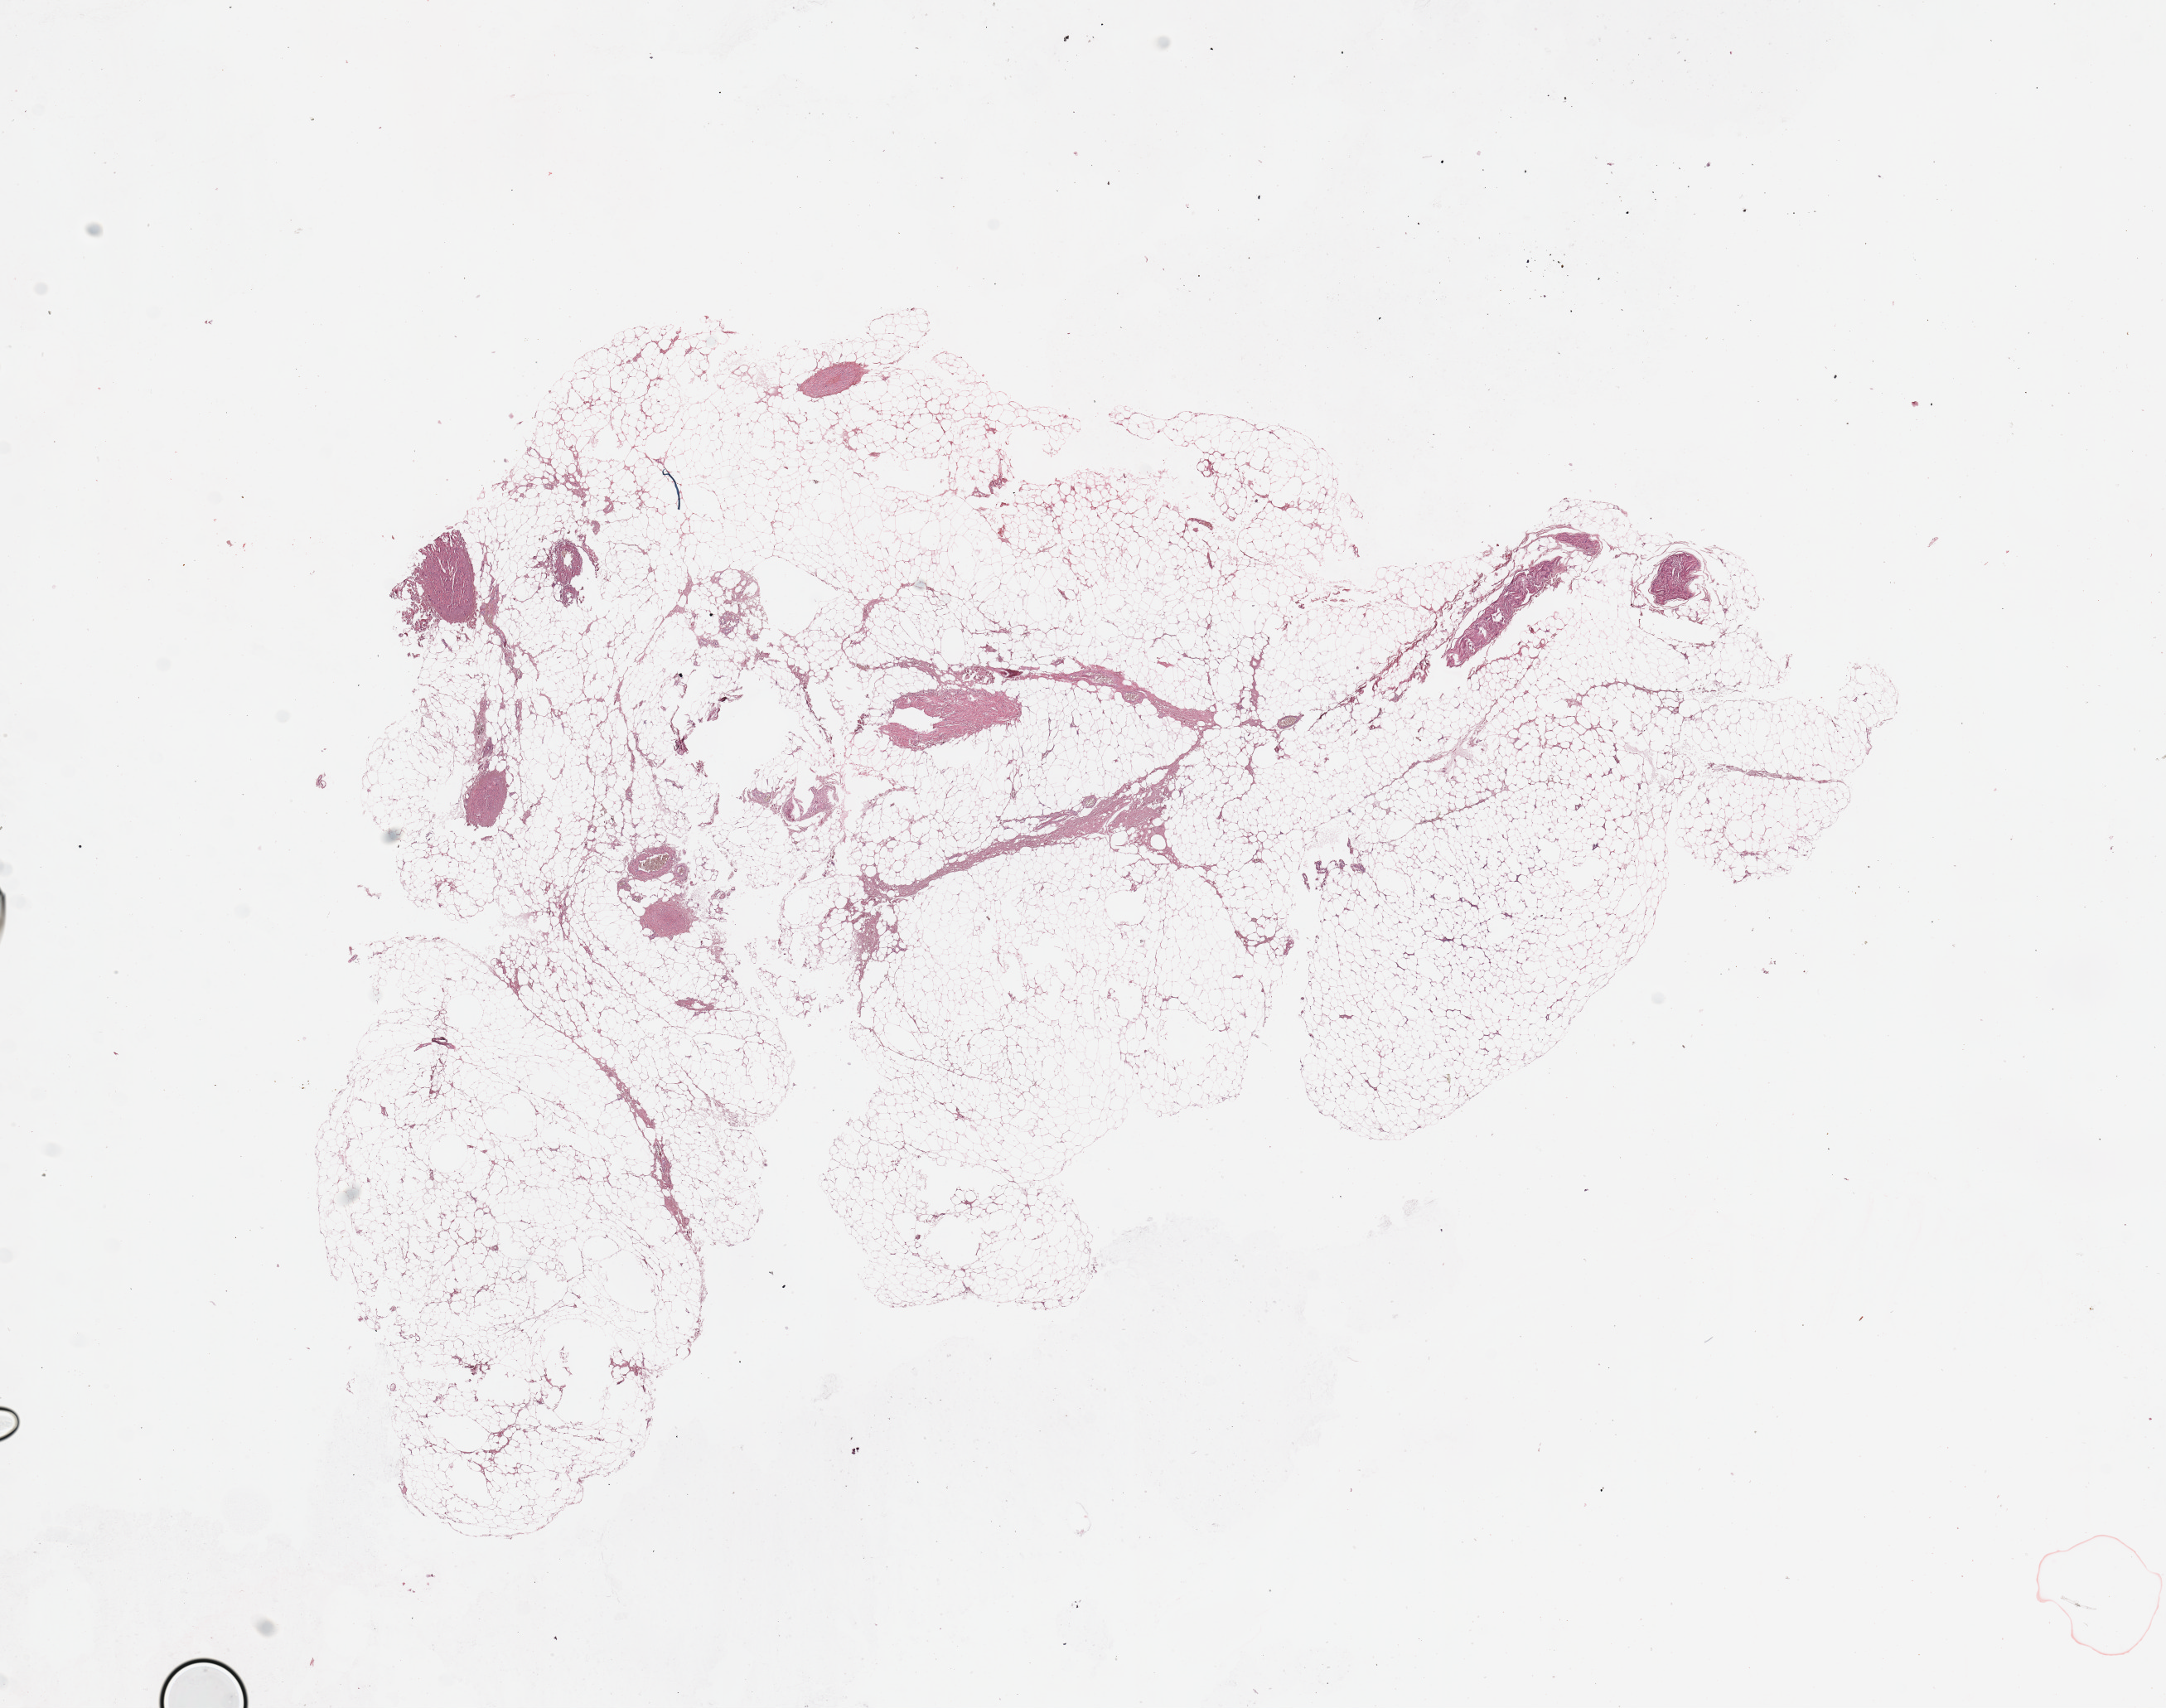
Hematoxylin and eosin (H&E) stained whole-slide image — a low-resolution overview of the entire scanned area, about 20.7 x 16.3 mm (from a 20x scan); normal (non-tumour) tissue sample, sampled site: skin. Patient: male, age 77 years.
* this section: normal (non-tumour) tissue from the same patient
* patient diagnosis: Malignant melanoma, NOS